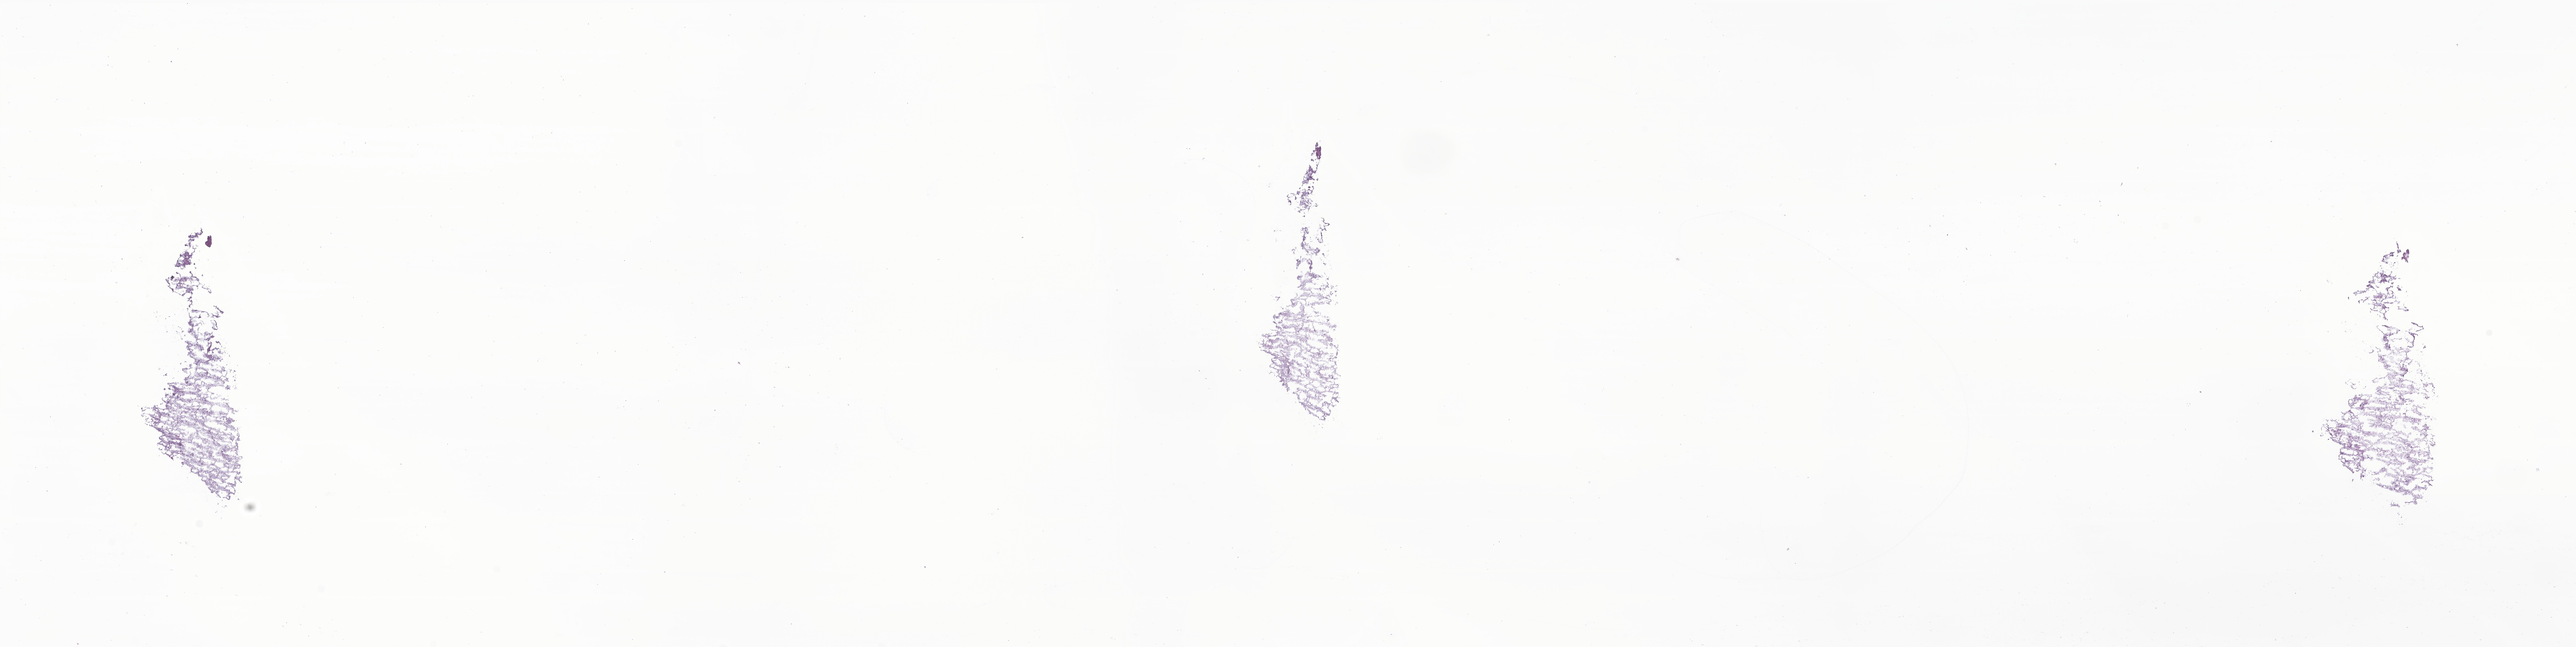
Whole-slide image, haematoxylin and eosin stain of tumor tissue from the brain, shown as a low-resolution overview of the whole scanned area (about 35.2 x 8.9 mm). Frozen section (OCT-embedded). Patient: female, age 282 days.
Recorded diagnosis: Pilocytic astrocytoma.